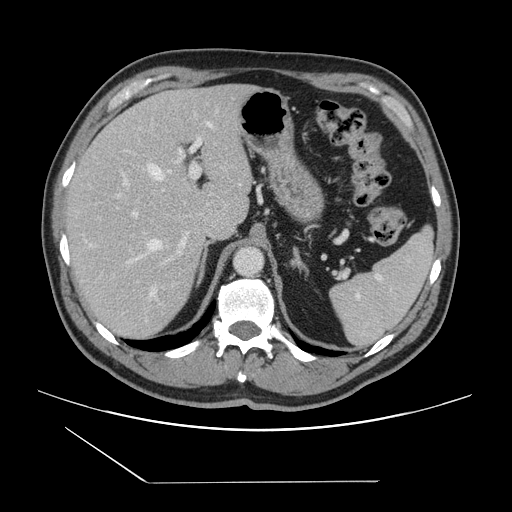
Contrast-enhanced abdominal CT, one axial slice. Slice 100 of 157 in the series (ordered by position). Intravenous contrast given. Soft-tissue window (W 400 / L 40 HU). 512 × 512 image matrix, field of view 407 × 407 mm. Male patient, age 61 years. Case-level facts recorded for this patient, not image findings: diagnosis: colorectal cancer liver metastases, imaged before liver resection; multiple liver metastases: yes; largest metastasis: 5.5 cm; disease in both lobes: yes.
Structures marked on this image (expert manual segmentation):
- hepatic veins: bounding box [x1, y1, x2, y2] px = [149, 123, 213, 297]
- liver: [66, 85, 251, 340]
- planned liver remnant (the part of the liver to remain after resection): [68, 85, 238, 223]
- portal vein (with intrahepatic branches): [90, 137, 202, 262]